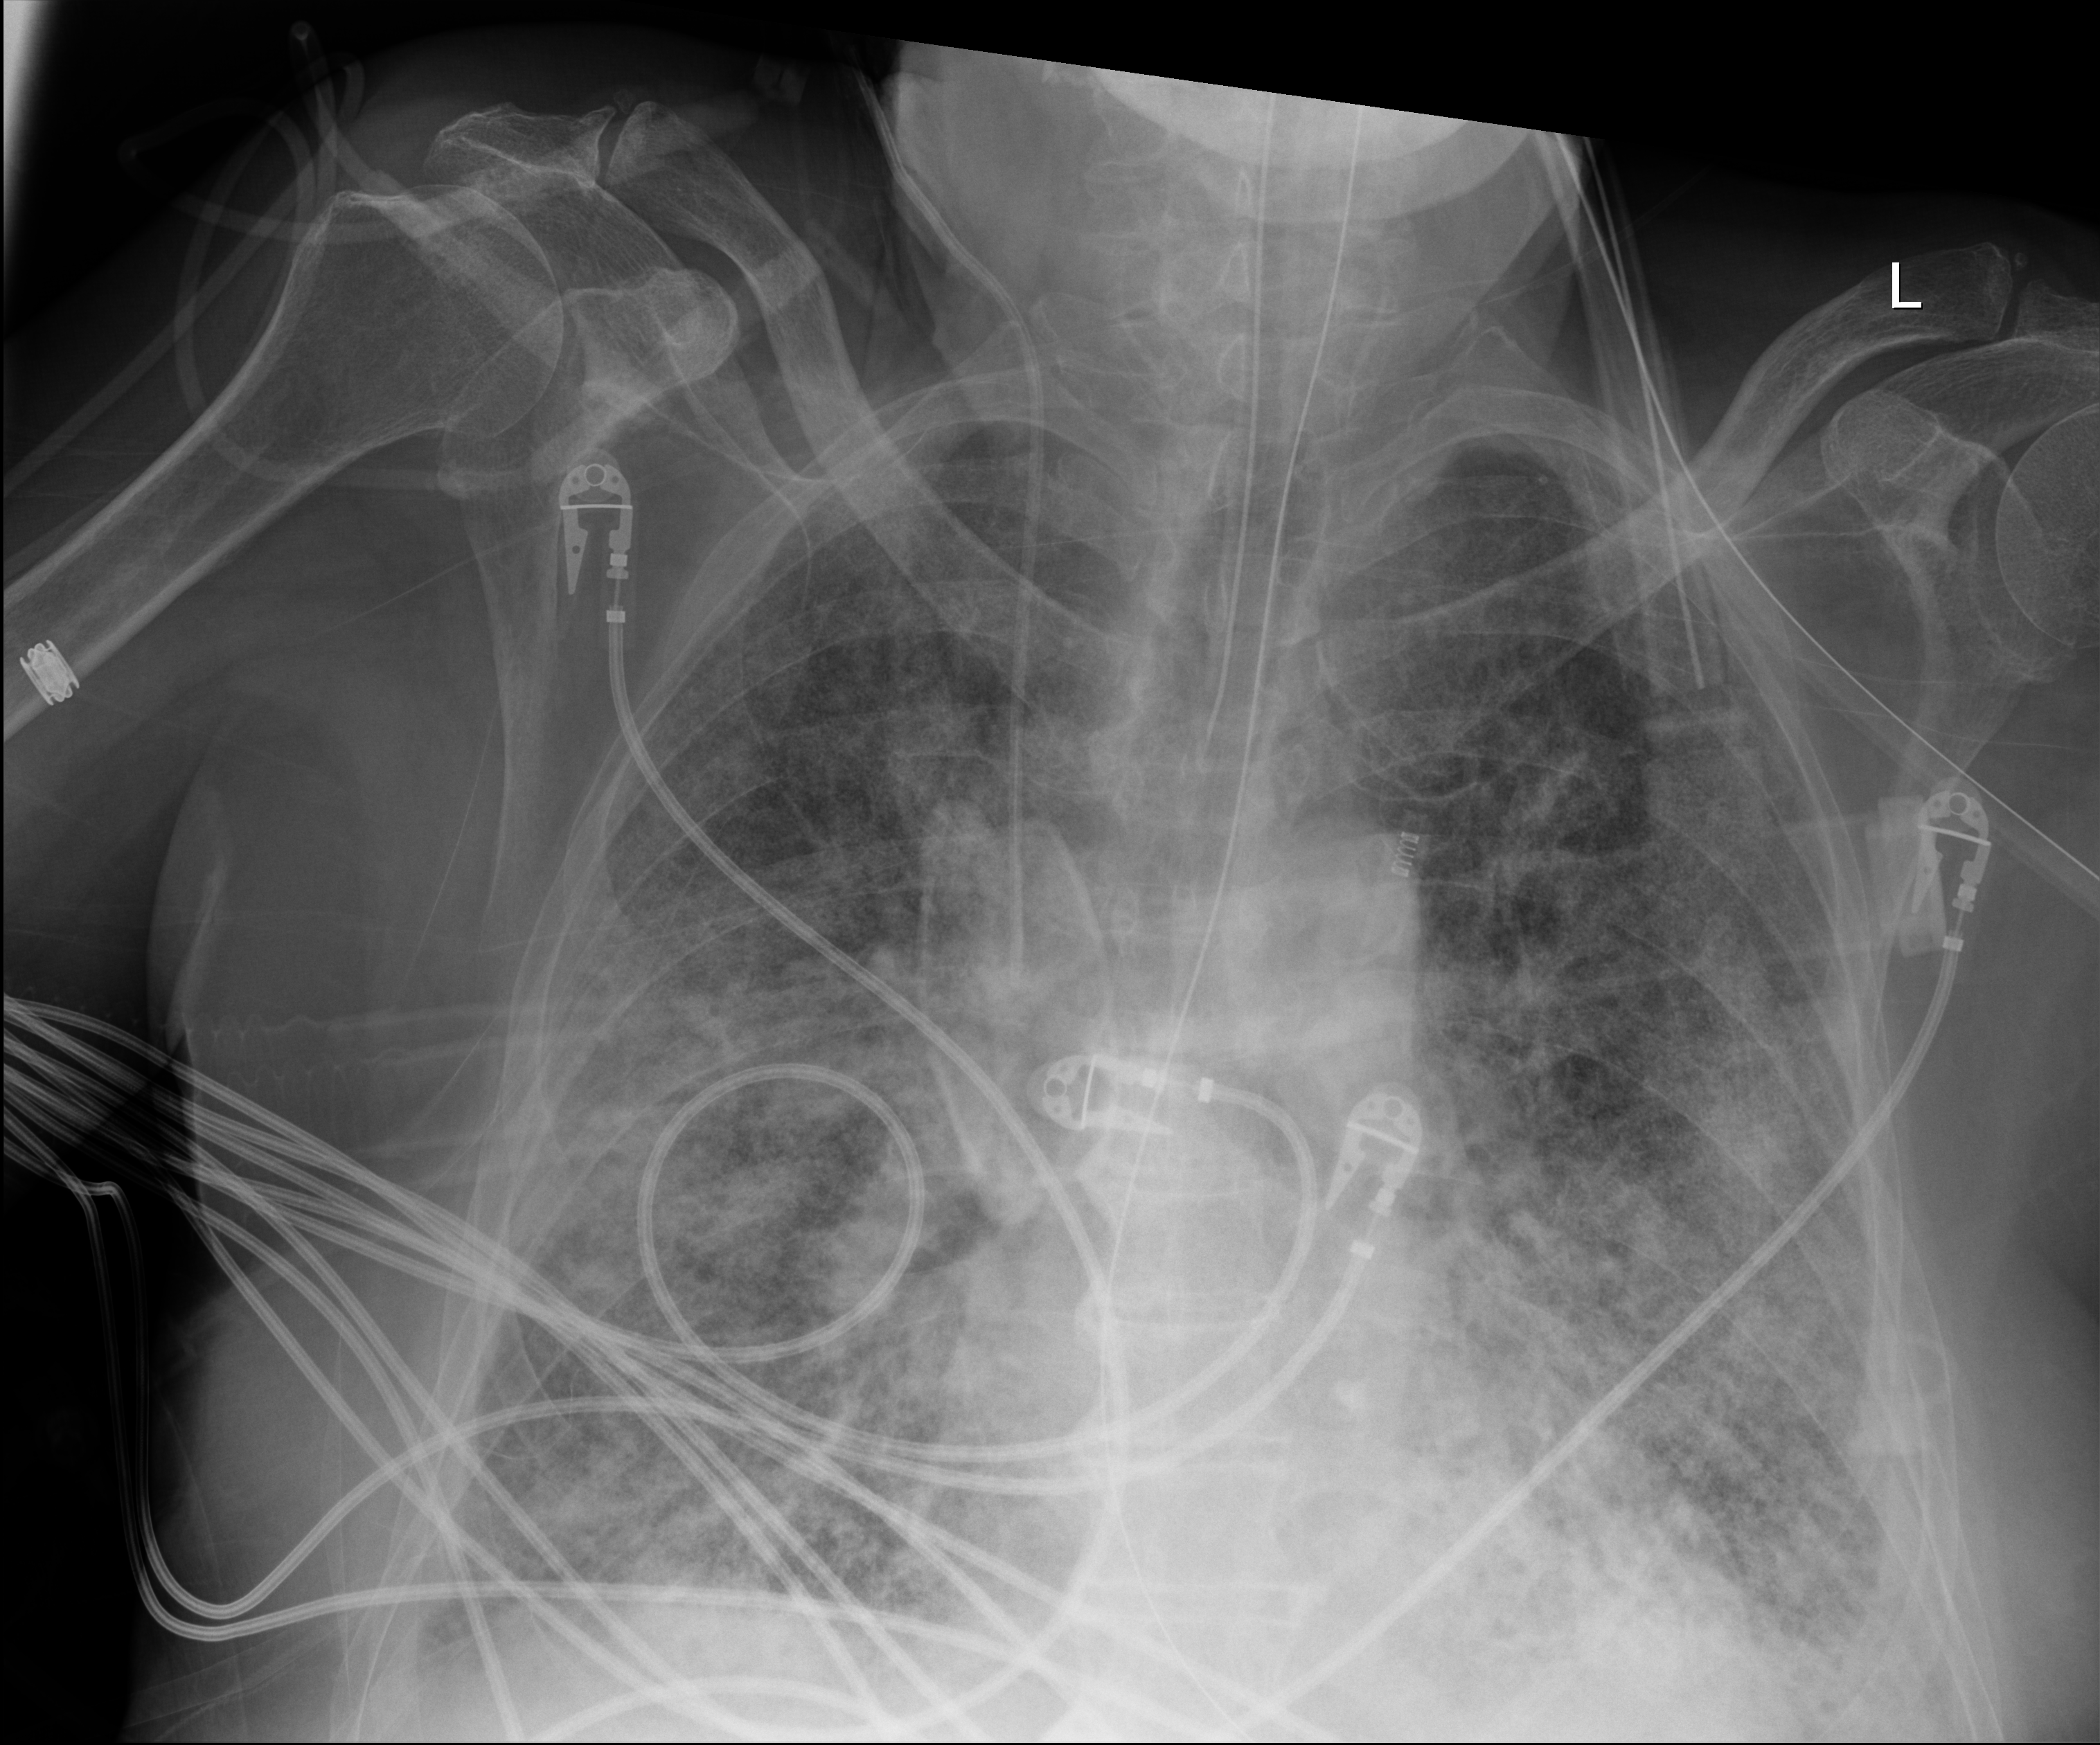
Bedside chest radiograph (digital radiography), anteroposterior (AP) projection. Male patient hospitalised with COVID-19, age 75–90 years.
From the hospital-stay record, not from the radiograph (when in the stay this image was taken is not recorded): diabetes (admission record): no; mechanically ventilated during this hospital stay: yes; length of hospital stay: 47 days.